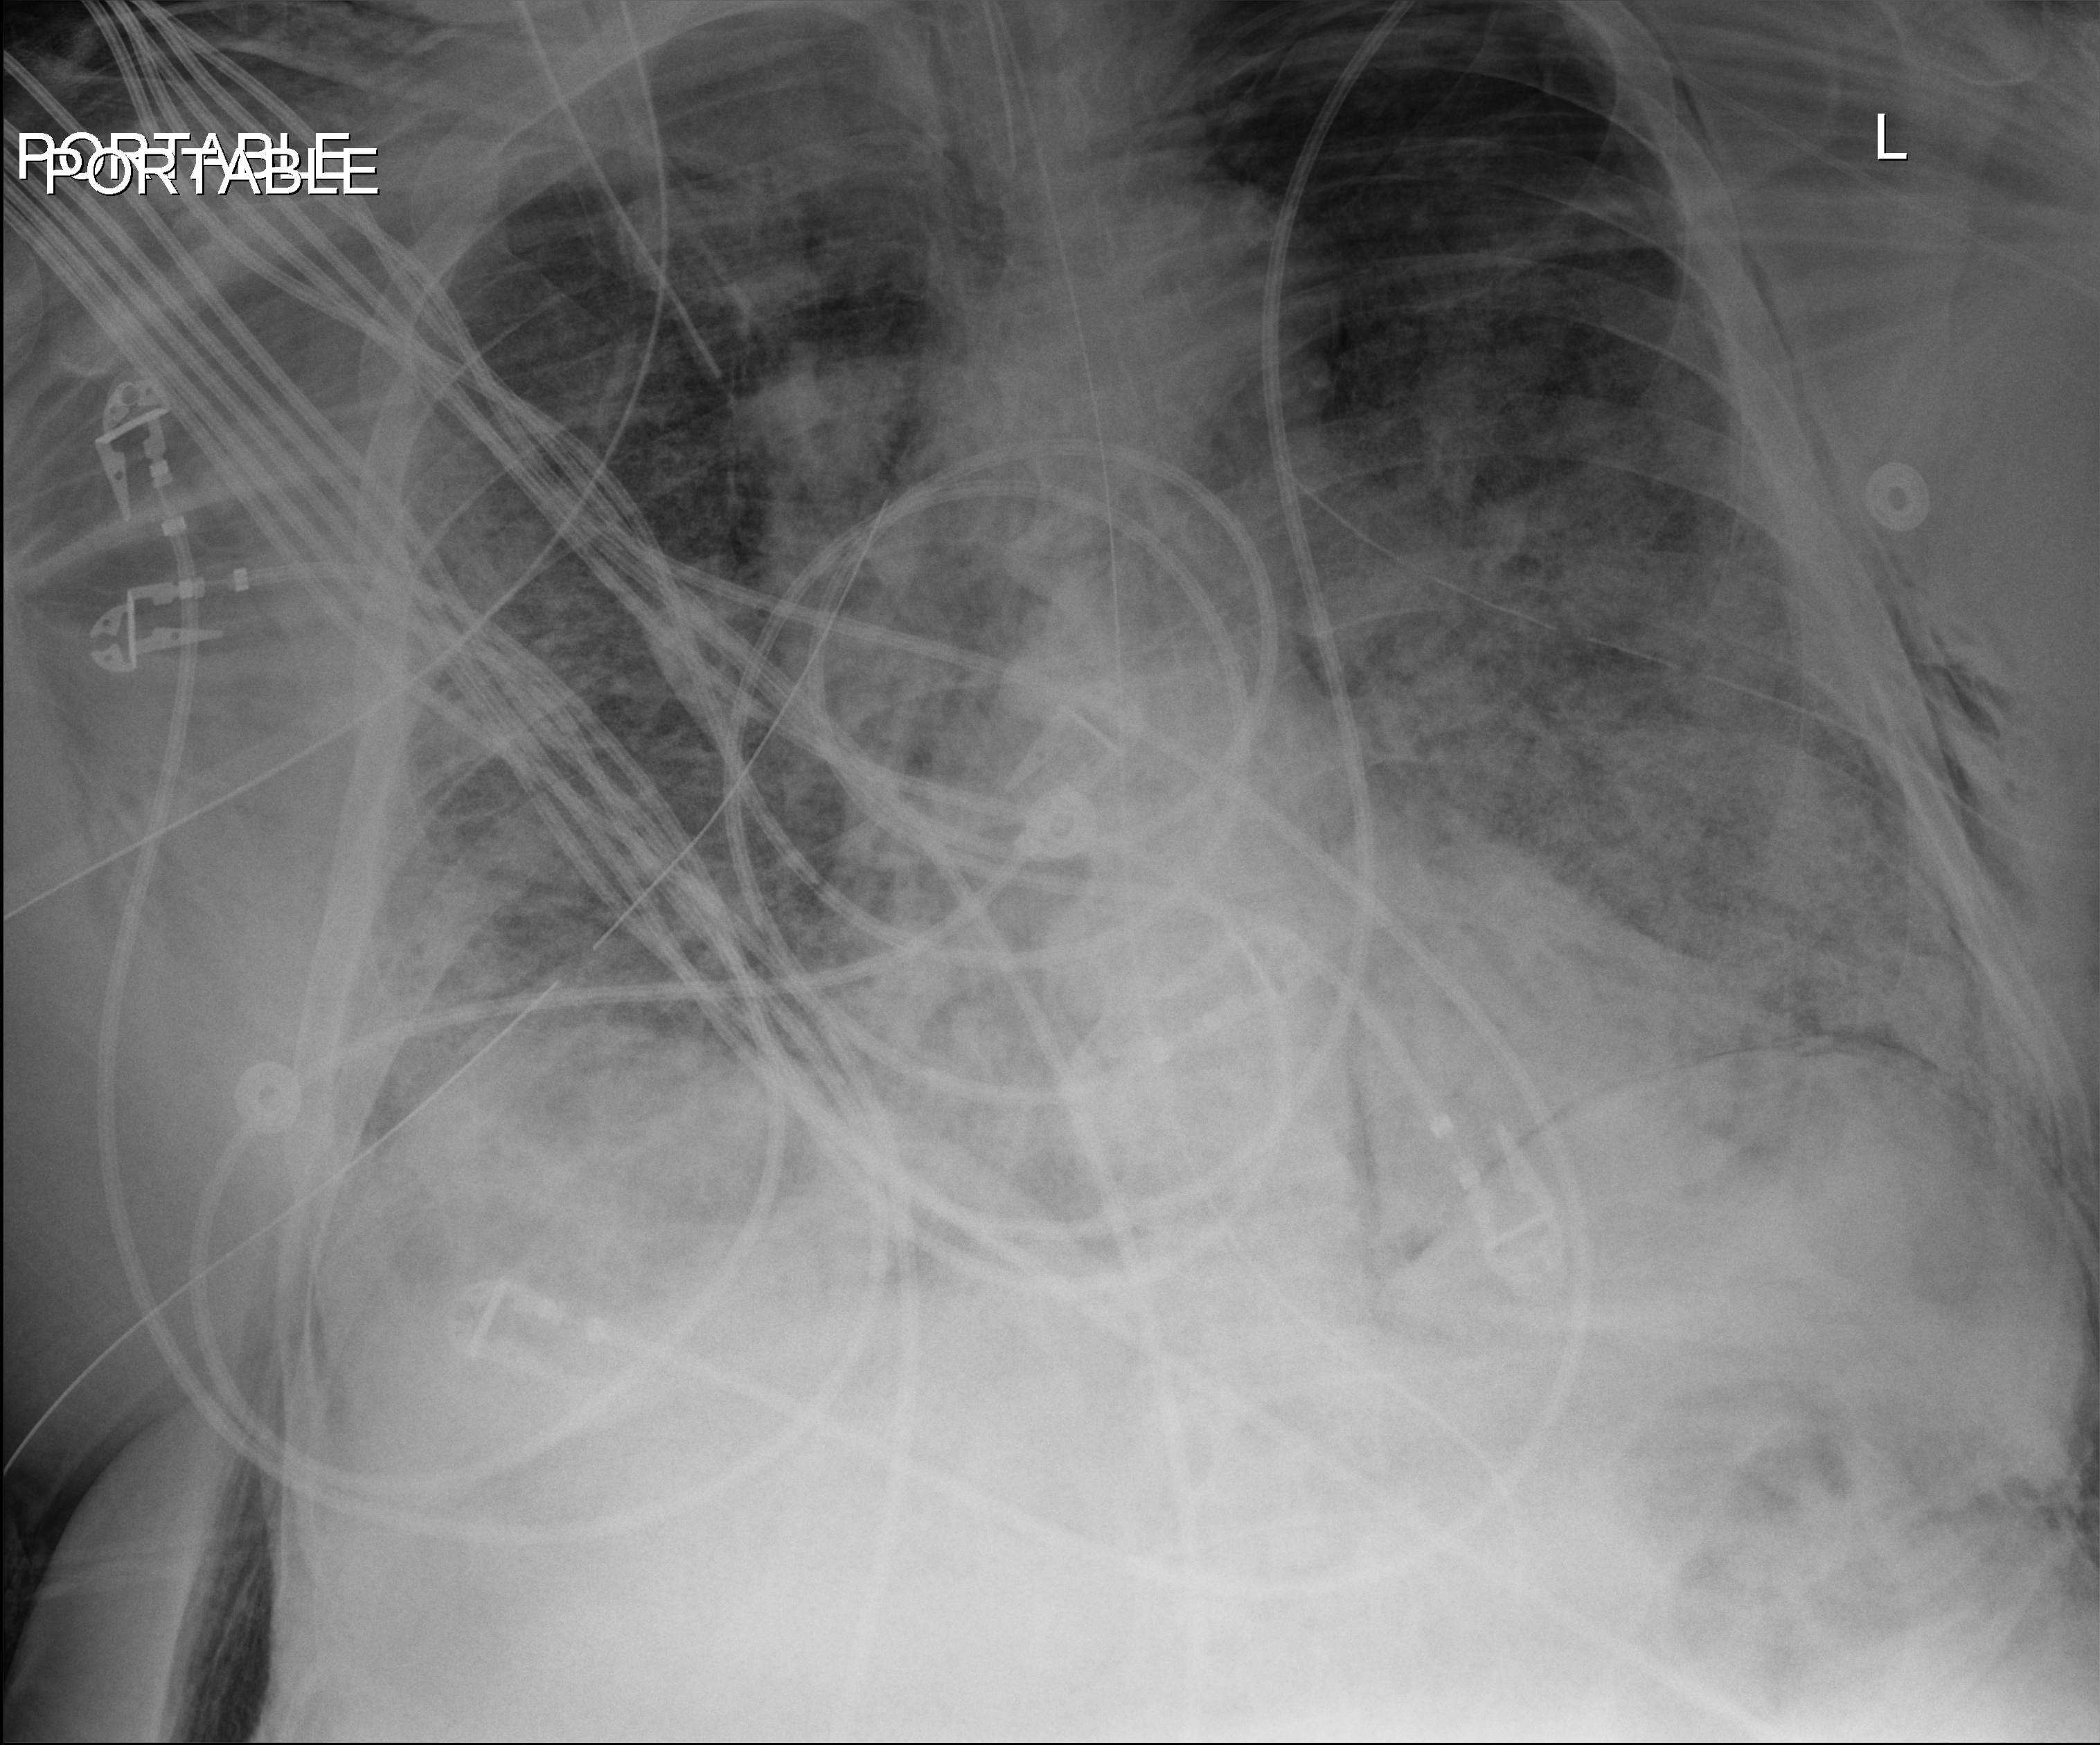
Chest radiograph. Adult patient hospitalised with COVID-19, age 18–59 years.
Hospital-stay facts (about this admission, not read from this image; timing relative to this image not recorded): COPD (admission record): no.